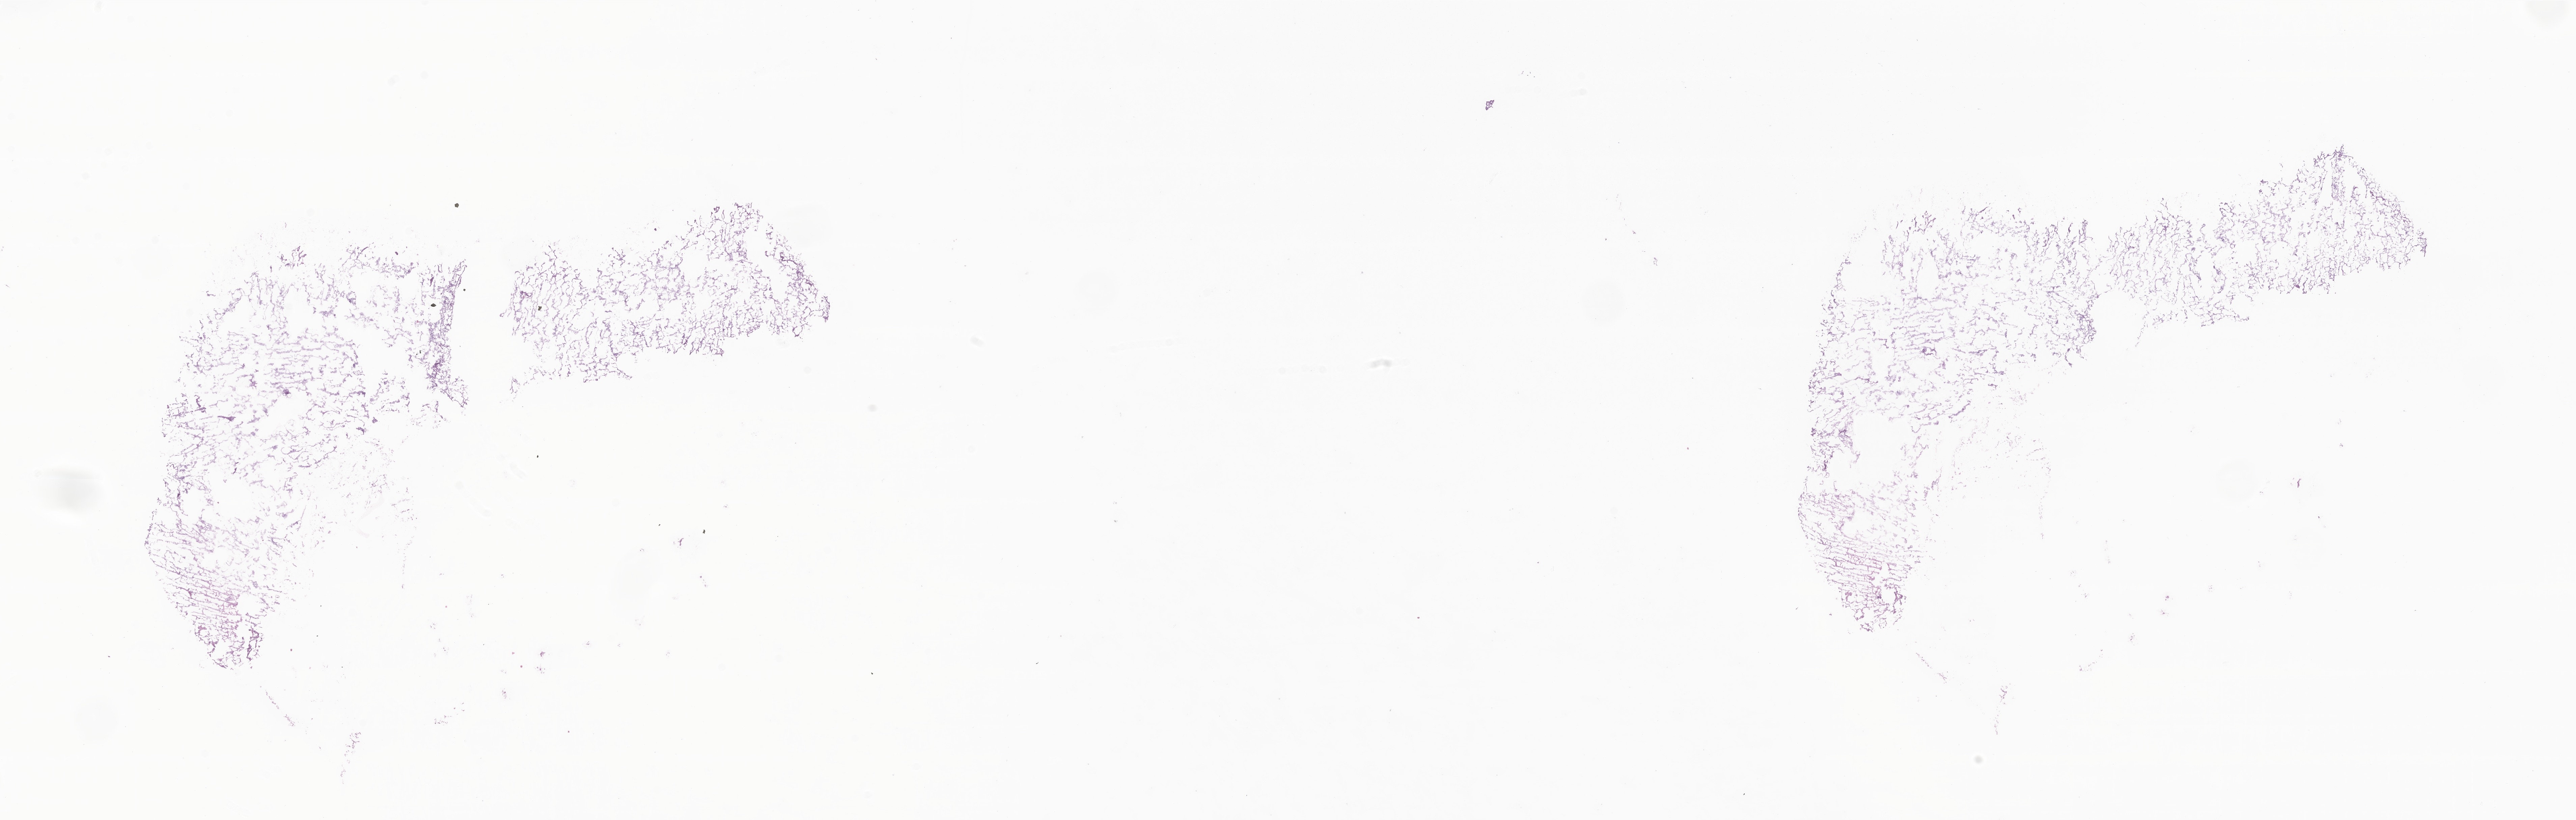
Haematoxylin and eosin whole-slide image of tumor tissue from the cerebellum — a low-resolution overview of the entire scanned area, about 32.2 x 10.2 mm. Frozen section. Patient male; age 34 months (2 years 10 months).
Diagnosis (ICD-O-3 morphology term): Pilocytic astrocytoma.